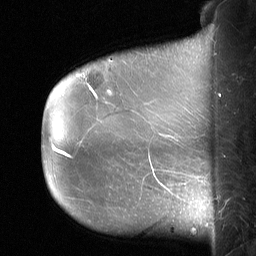
Breast MRI (dynamic contrast-enhanced), one sagittal slice; slice 15 of 64 in the series (ordered by position); dynamic contrast-enhanced study with each time point stored as its own series, time point 2 of 3 at this slice position (early post-contrast, ordered by acquisition time); 1.5 T; TE 4.8 ms, TR 27 ms; 256 × 256 image matrix. Female patient, age 60 years. From the clinical record (not read from this slice): setting: breast cancer imaged before/during neoadjuvant chemotherapy; receptor status: HR-positive, HER2-negative.
Outlined on this slice (semi-automatically segmented with operator editing):
- analysis volume of interest (the breast-tissue region the enhancement analysis was run in; not a lesion): bounding box (x1, y1, x2, y2) in pixels: (79, 55, 122, 99)
- tumour enhancement mask (voxels above the 90 % enhancement threshold inside the analysis volume of interest): (90, 87, 96, 96)